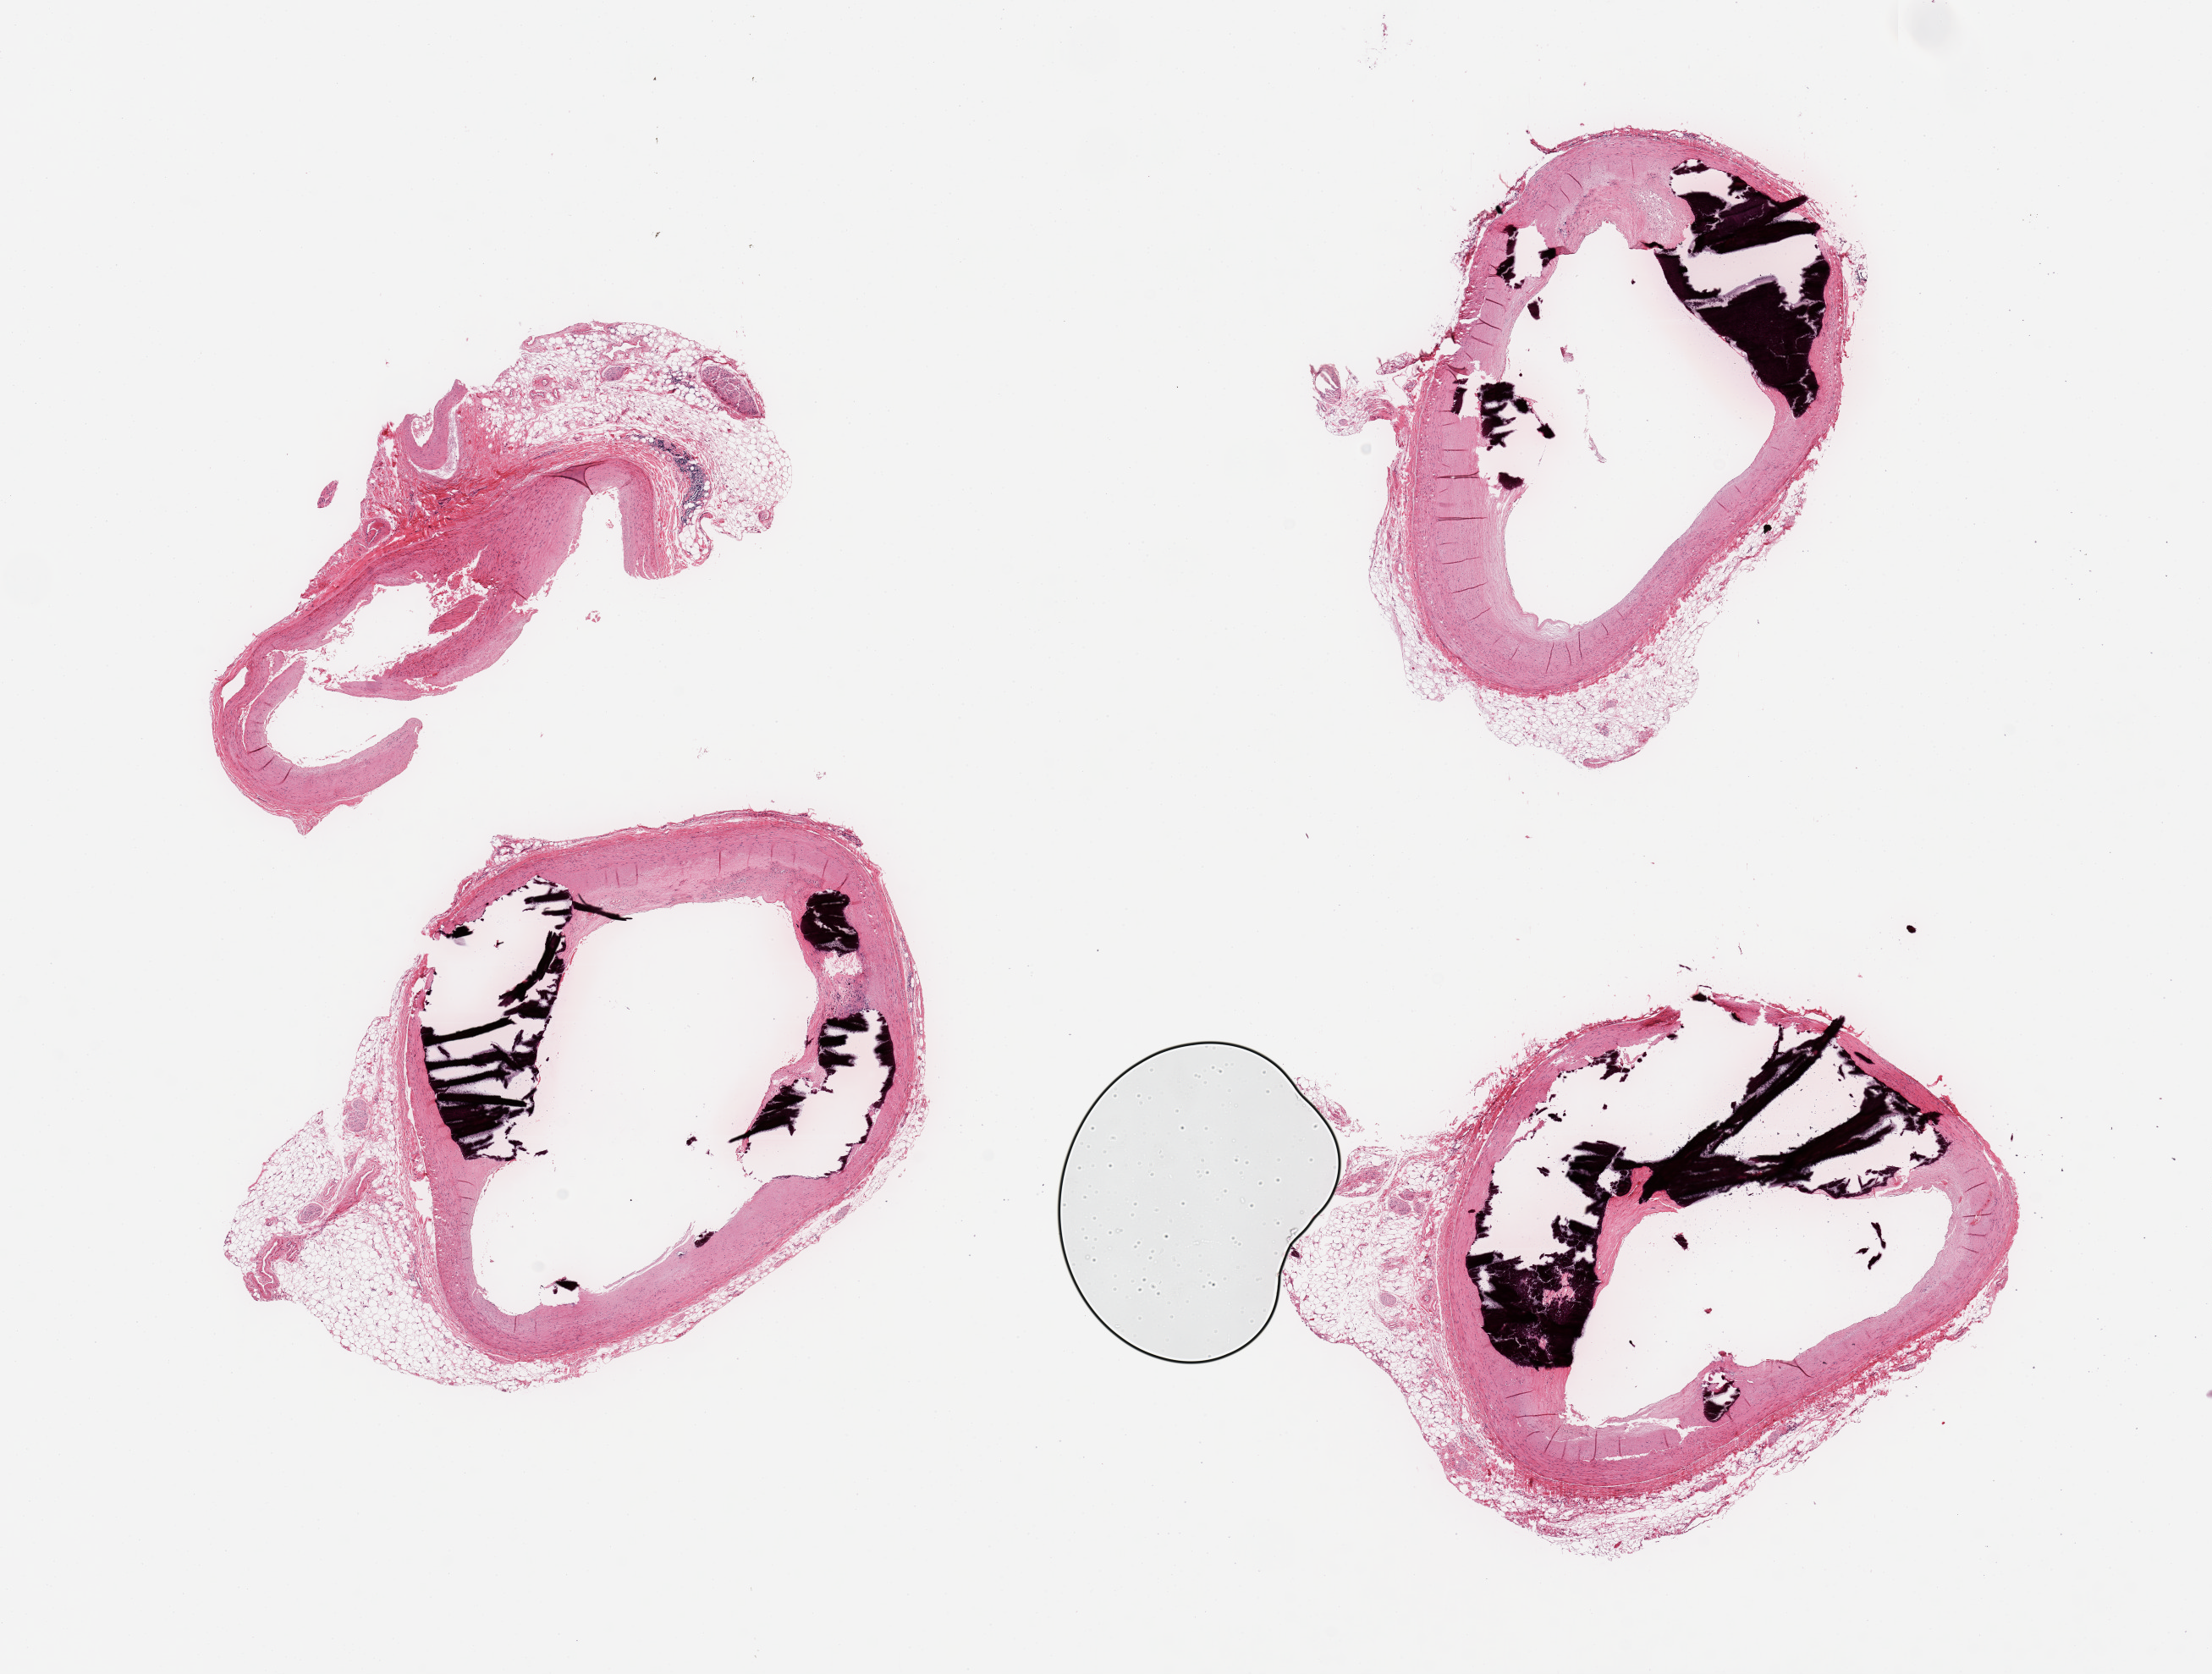
H&E whole-slide image, shown as a low-resolution overview of the whole scanned area (about 20.7 x 15.6 mm), PAXgene-fixed paraffin-embedded (PFPE) section, target tissue: coronary artery, donor tissue sample. Donor sex: male.
Reviewer comment on this tissue sample: 4 pieces, calcified atherosis with ~50% luminal obstruction; adherent nubbins of fat up to ~2mm.